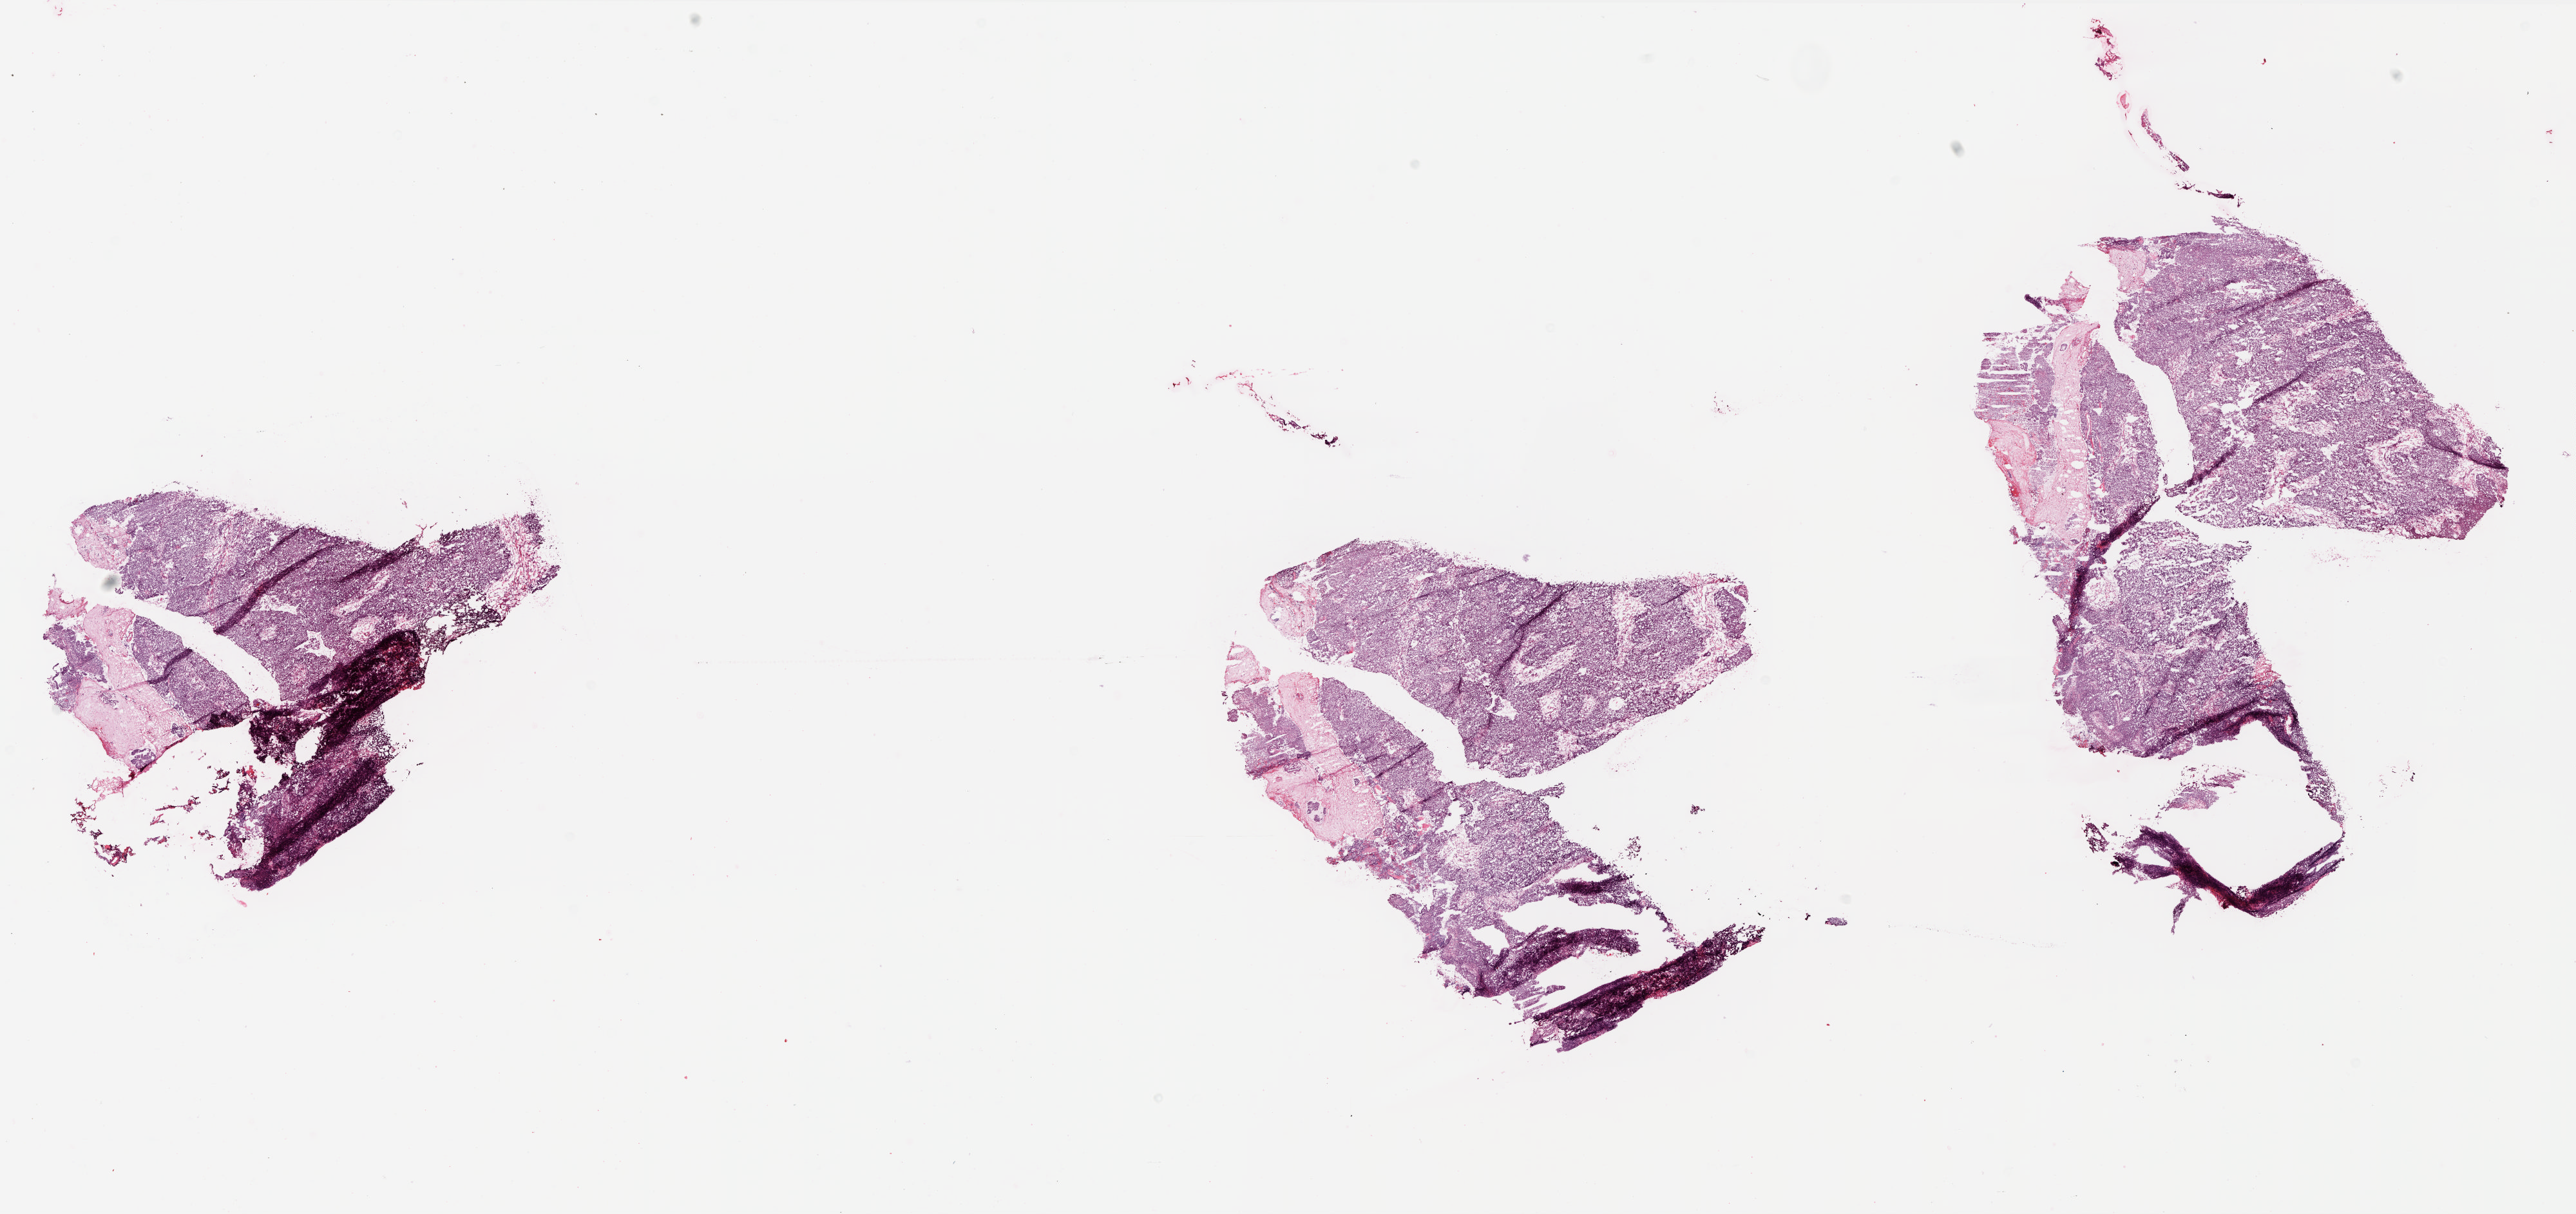
Digitized H&E-stained tissue section (whole slide), a low-resolution overview of the entire scanned area, about 31.9 x 15.1 mm. Frozen section. Primary tumour sample from the ovary. Female patient; age at initial diagnosis 52 years. Histologic grade: G3 (poorly differentiated). Slide review estimates, as recorded: tumour cells 80%, tumour nuclei 90%, normal cells 0%, stromal cells 15%, necrosis 5%.
• histologic diagnosis: Serous cystadenocarcinoma, NOS
• laterality: bilateral
• FIGO stage: IIIC